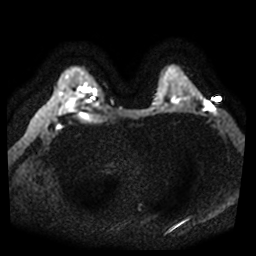
Breast MRI, one axial slice. Position 31 of 44 along the scan axis. Diffusion-weighted series; image 2 of 4 stored at this slice position (different b-values; order by instance number). 3 T. 5 mm slice thickness. 256 × 256 image matrix, field of view 360 × 360 mm. Female patient.
Annotated regions visible in this slice (outlined manually by an expert reader):
- tumour on diffusion-weighted imaging: bounding box [x1, y1, x2, y2] px = [211, 107, 215, 111]